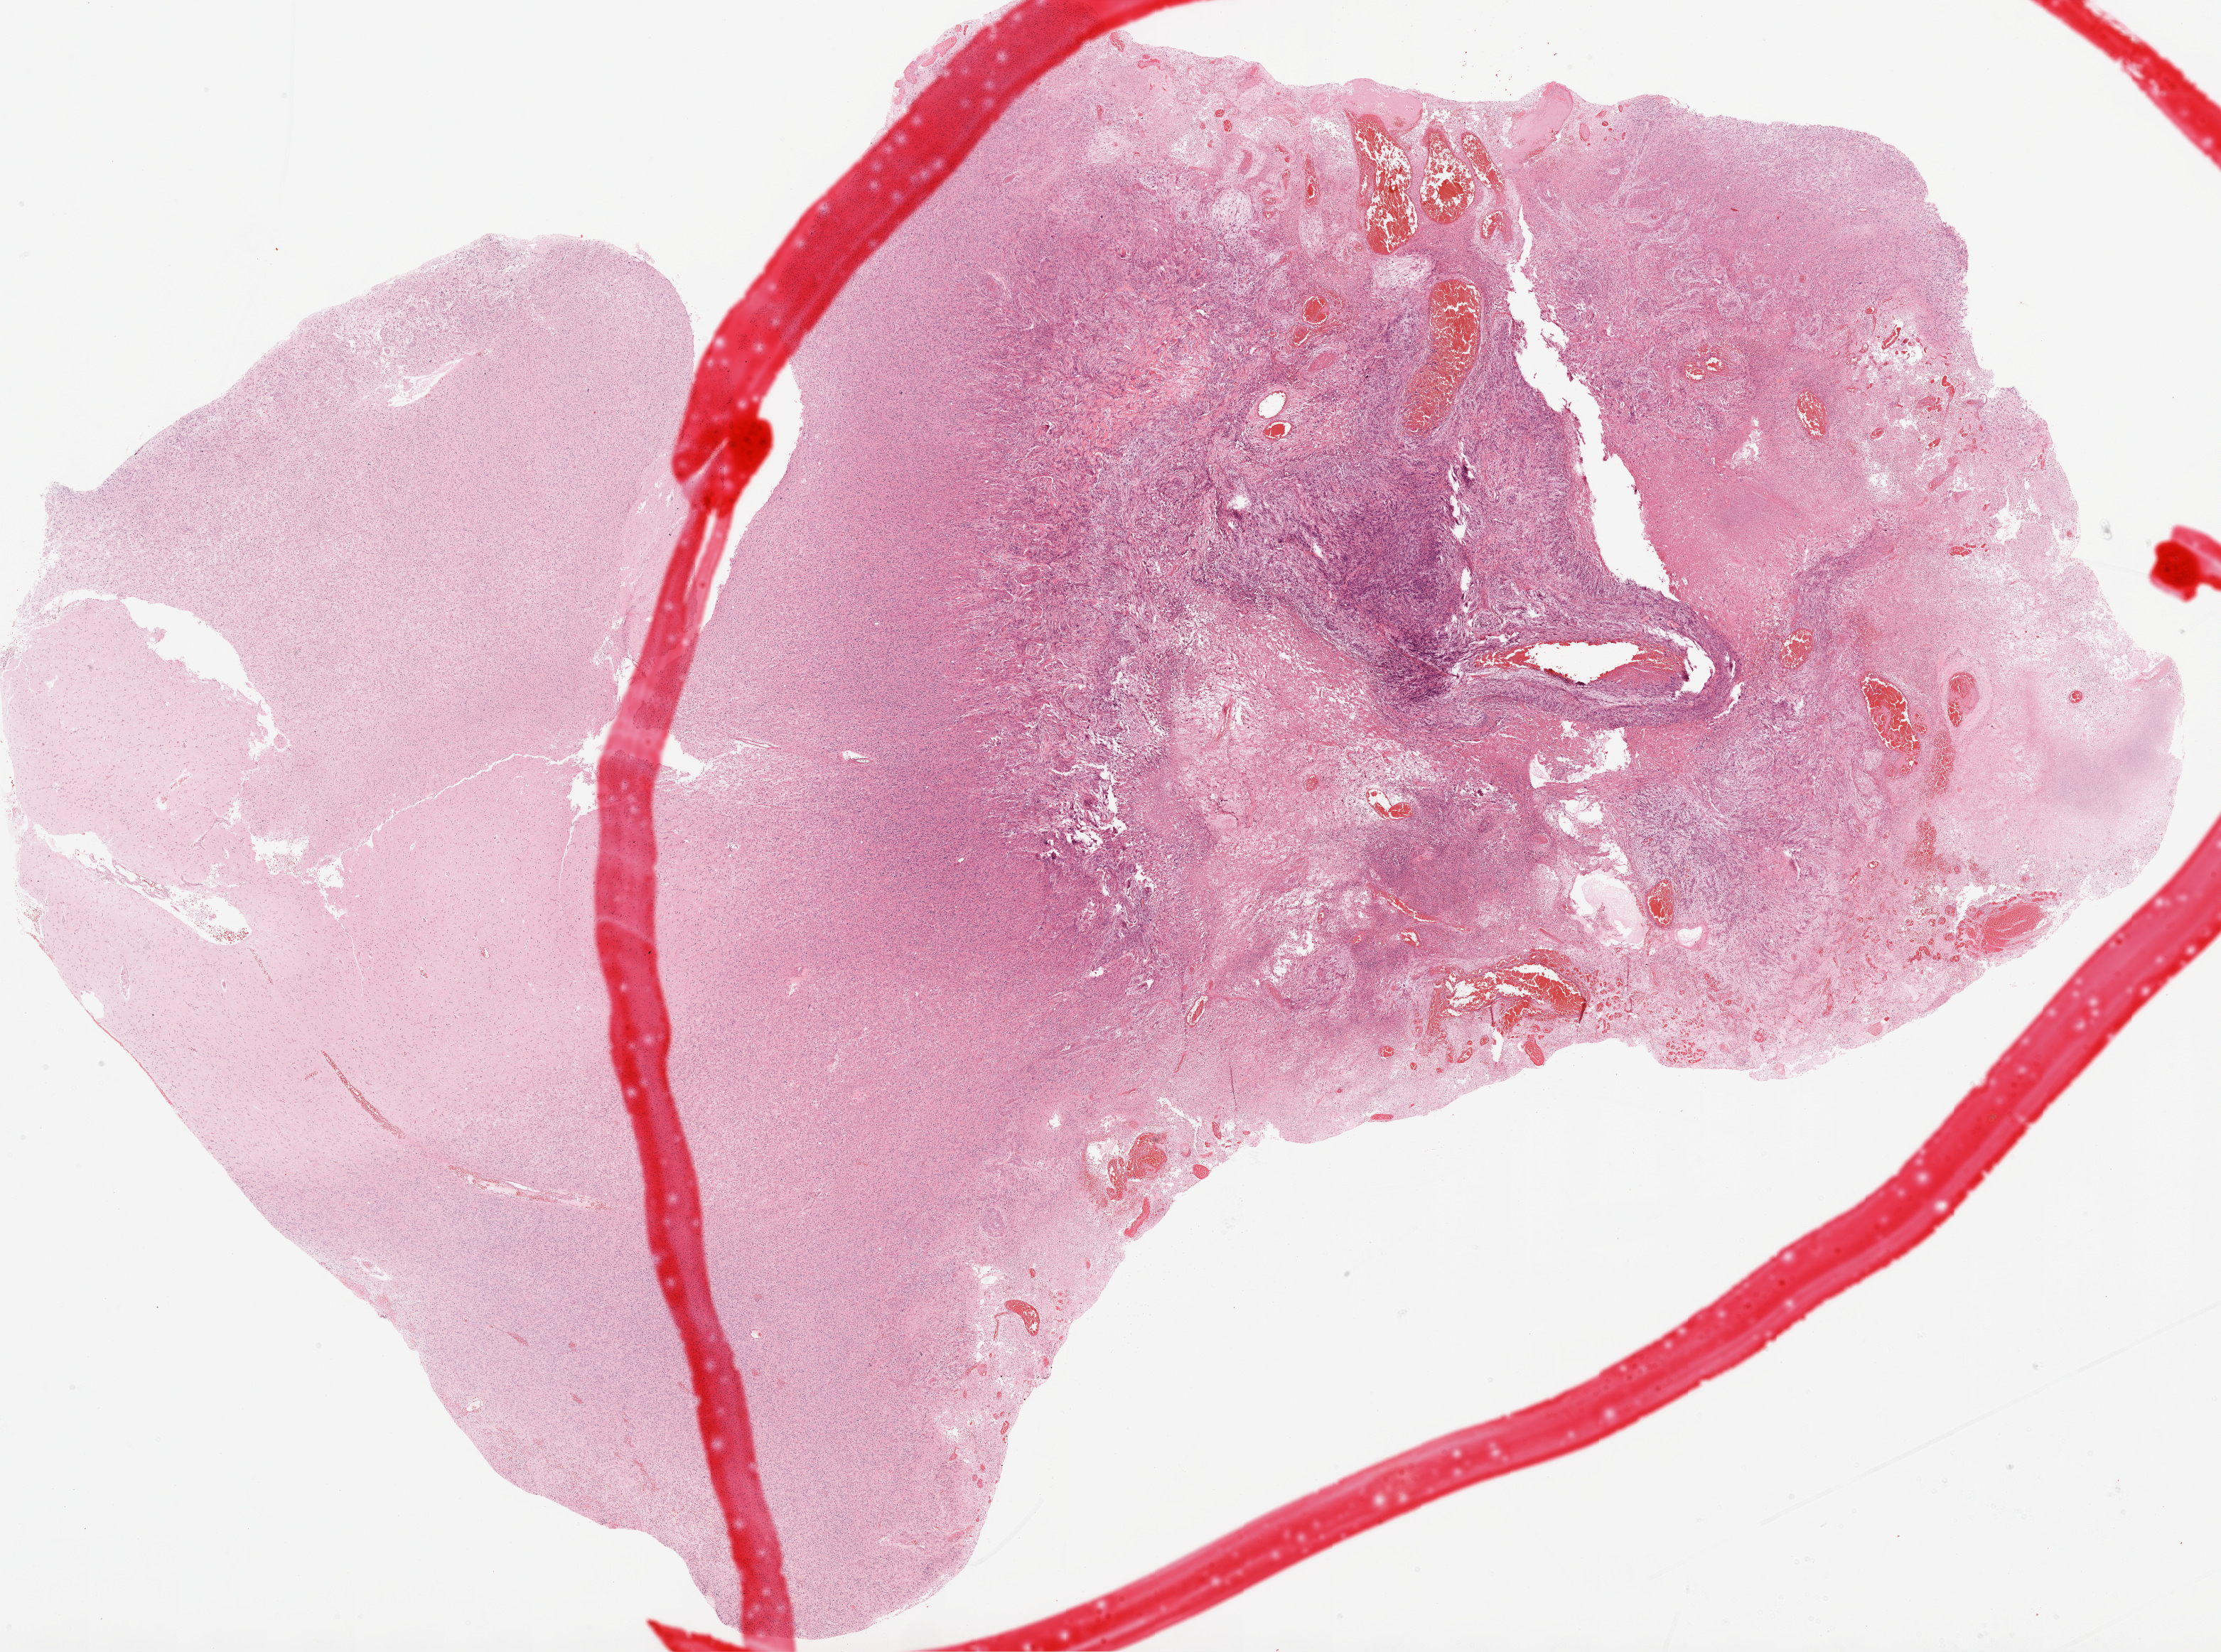
Digitized Hematoxylin and eosin (H&E) stained tissue section (whole slide) — a low-resolution overview of the entire scanned area, about 25.1 x 18.7 mm. Formalin-fixed paraffin-embedded (FFPE) diagnostic section. Sample: primary tumour, brain. Male, age 60 years at initial diagnosis.
Histologic diagnosis: Glioblastoma.